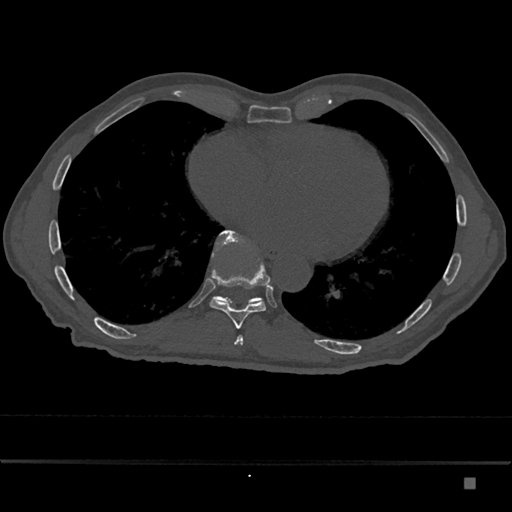
CT including the spine, one axial slice. Position 789 of 797 along the scan axis. Reconstruction kernel Br40s/3. Bone window (W 1800 / L 400 HU). 0.5 mm slice thickness. 512 × 512 image matrix, field of view 390 × 390 mm. Patient: male, 72 years. Case-level facts recorded for this patient, not image findings: primary cancer: prostate.
Structures marked on this image (semi-automatically segmented with operator editing):
- T10 vertebra: bounding box [x1, y1, x2, y2] px = [212, 230, 263, 304]
- T9 vertebra: [210, 230, 270, 329]